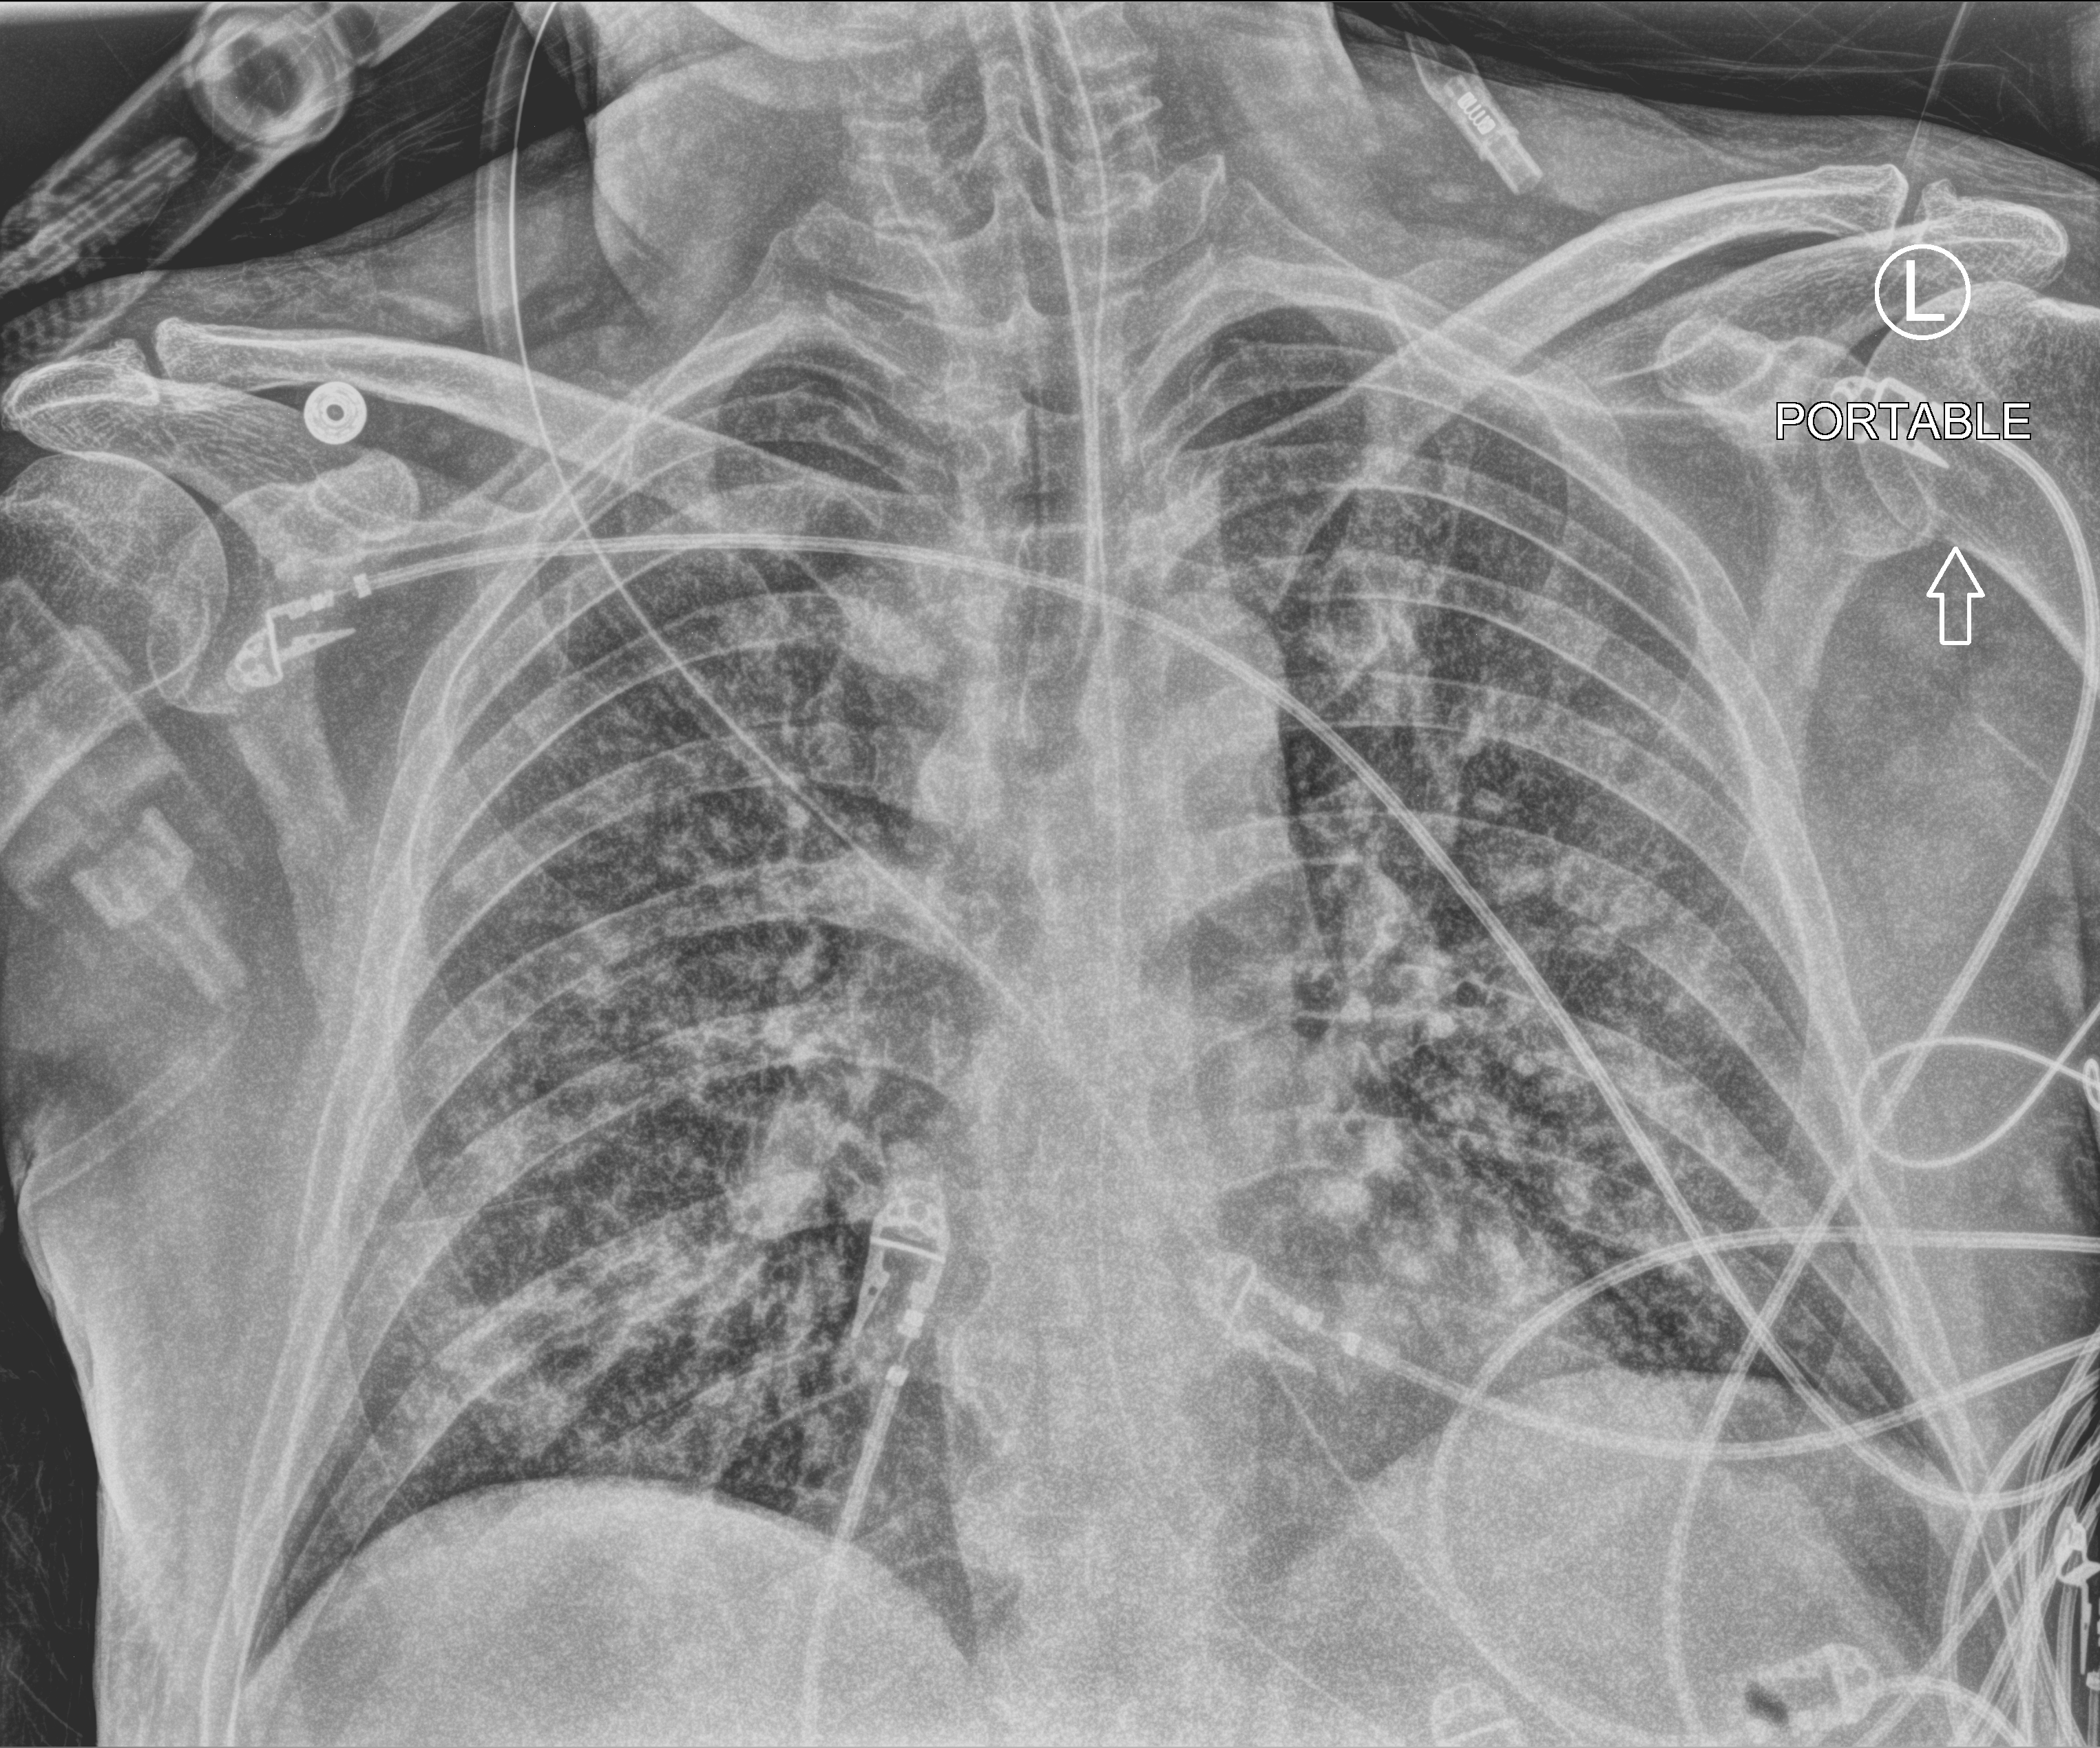
Portable chest radiograph; anteroposterior (AP) projection. Patient hospitalised with COVID-19; male, aged 18–59 years.
Admission-level facts for this patient (not findings on this image; timing relative to this image not recorded): length of hospital stay: 19 days; mechanically ventilated during this hospital stay: yes.